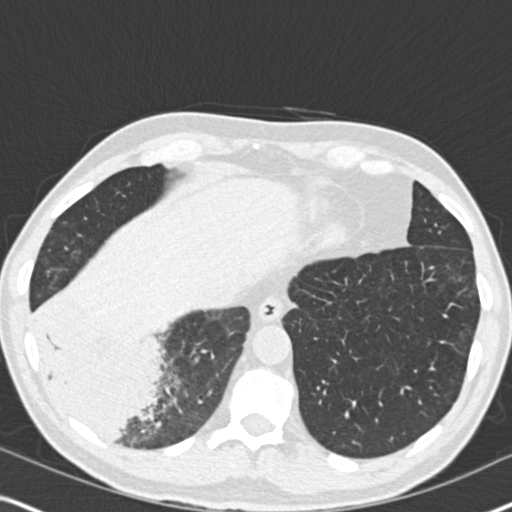
Low-dose screening chest CT, one axial slice; slice 55 of 182 in the series (ordered by position); 120 kVp; lung window (W 1500 / L -600 HU); 512 × 512 image matrix.
Outlined on this slice (expert manual segmentation):
- lesion 1 (tumor, lower lobe of right lung): bounding box <41,325,160,437> (left, top, right, bottom; pixels)